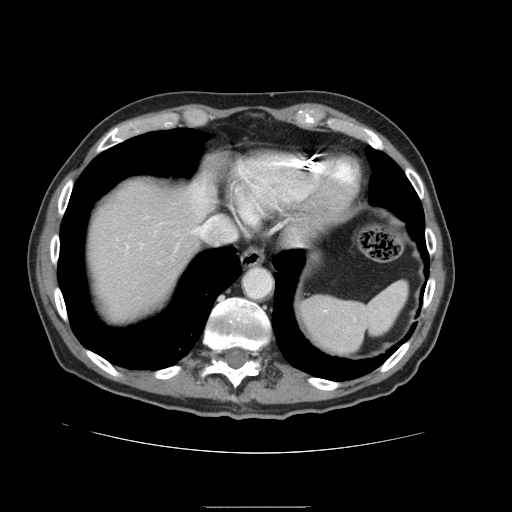
Contrast-enhanced abdominal CT, one axial slice; slice 132 of 168 in the series (ordered by position); intravenous contrast given; soft-tissue window (W 400 / L 40 HU); 2.5 mm slice thickness; 512 × 512 image matrix, field of view 386 × 386 mm. Male patient, age 74 years. From the clinical record (not read from this slice): diagnosis: colorectal cancer liver metastases, imaged before liver resection.
Structures marked on this image (expert manual segmentation):
- liver: bounding box (x1, y1, x2, y2) in pixels: (86, 177, 215, 325)
- planned liver remnant (the part of the liver to remain after resection): (86, 175, 216, 326)